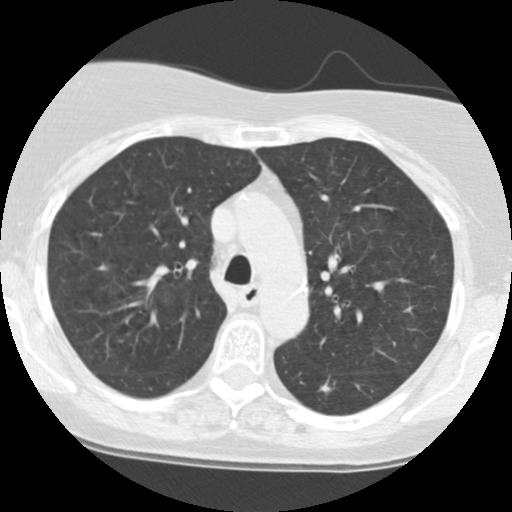
Axial slice from a low-dose chest CT screening exam, baseline annual screen, lung window (W 1500 / L -600 HU), 2.5 mm slice thickness, 120 kVp, slice 36 of 123 in the series, 512 × 512 image matrix. Female, age 63 years at enrolment. Current smoker at enrolment.
• Expert reader's lesion annotation, bounding box (x1, y1, x2, y2) in pixels: (297, 365, 353, 410).
• The screening reader recorded 2 non-calcified nodules or masses ≥4 mm on this exam; which of them this box marks is not recorded.
• Official screen result: positive, change unspecified: nodule(s) >= 4 mm or enlarging nodule(s), mass(es), or other non-specific abnormalities suspicious for lung cancer.
• Later outcome: lung cancer diagnosed 796 days after this screen — squamous cell carcinoma, NOS, left lower lobe, moderately differentiated (G2), stage IB (AJCC 6th edition), 15 mm at pathology.